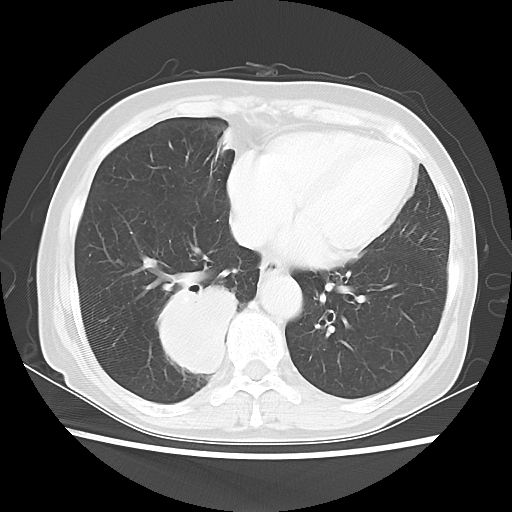
Chest CT, one axial slice. Slice 19 of 56 in the series (ordered by position). 120 kVp. Lung window (W 1500 / L -600 HU). 5 mm slice thickness. 512 × 512 image matrix. Patient: female, 66 years. Case-level facts recorded for this patient, not image findings: clinical TNM (as recorded): T2 N3 M0; histopathological grade: G3.
Annotated regions visible in this slice (bounding box drawn by a radiologist):
- lung tumour (recorded histology: small cell carcinoma): bounding box <122,264,240,384> (left, top, right, bottom; pixels)